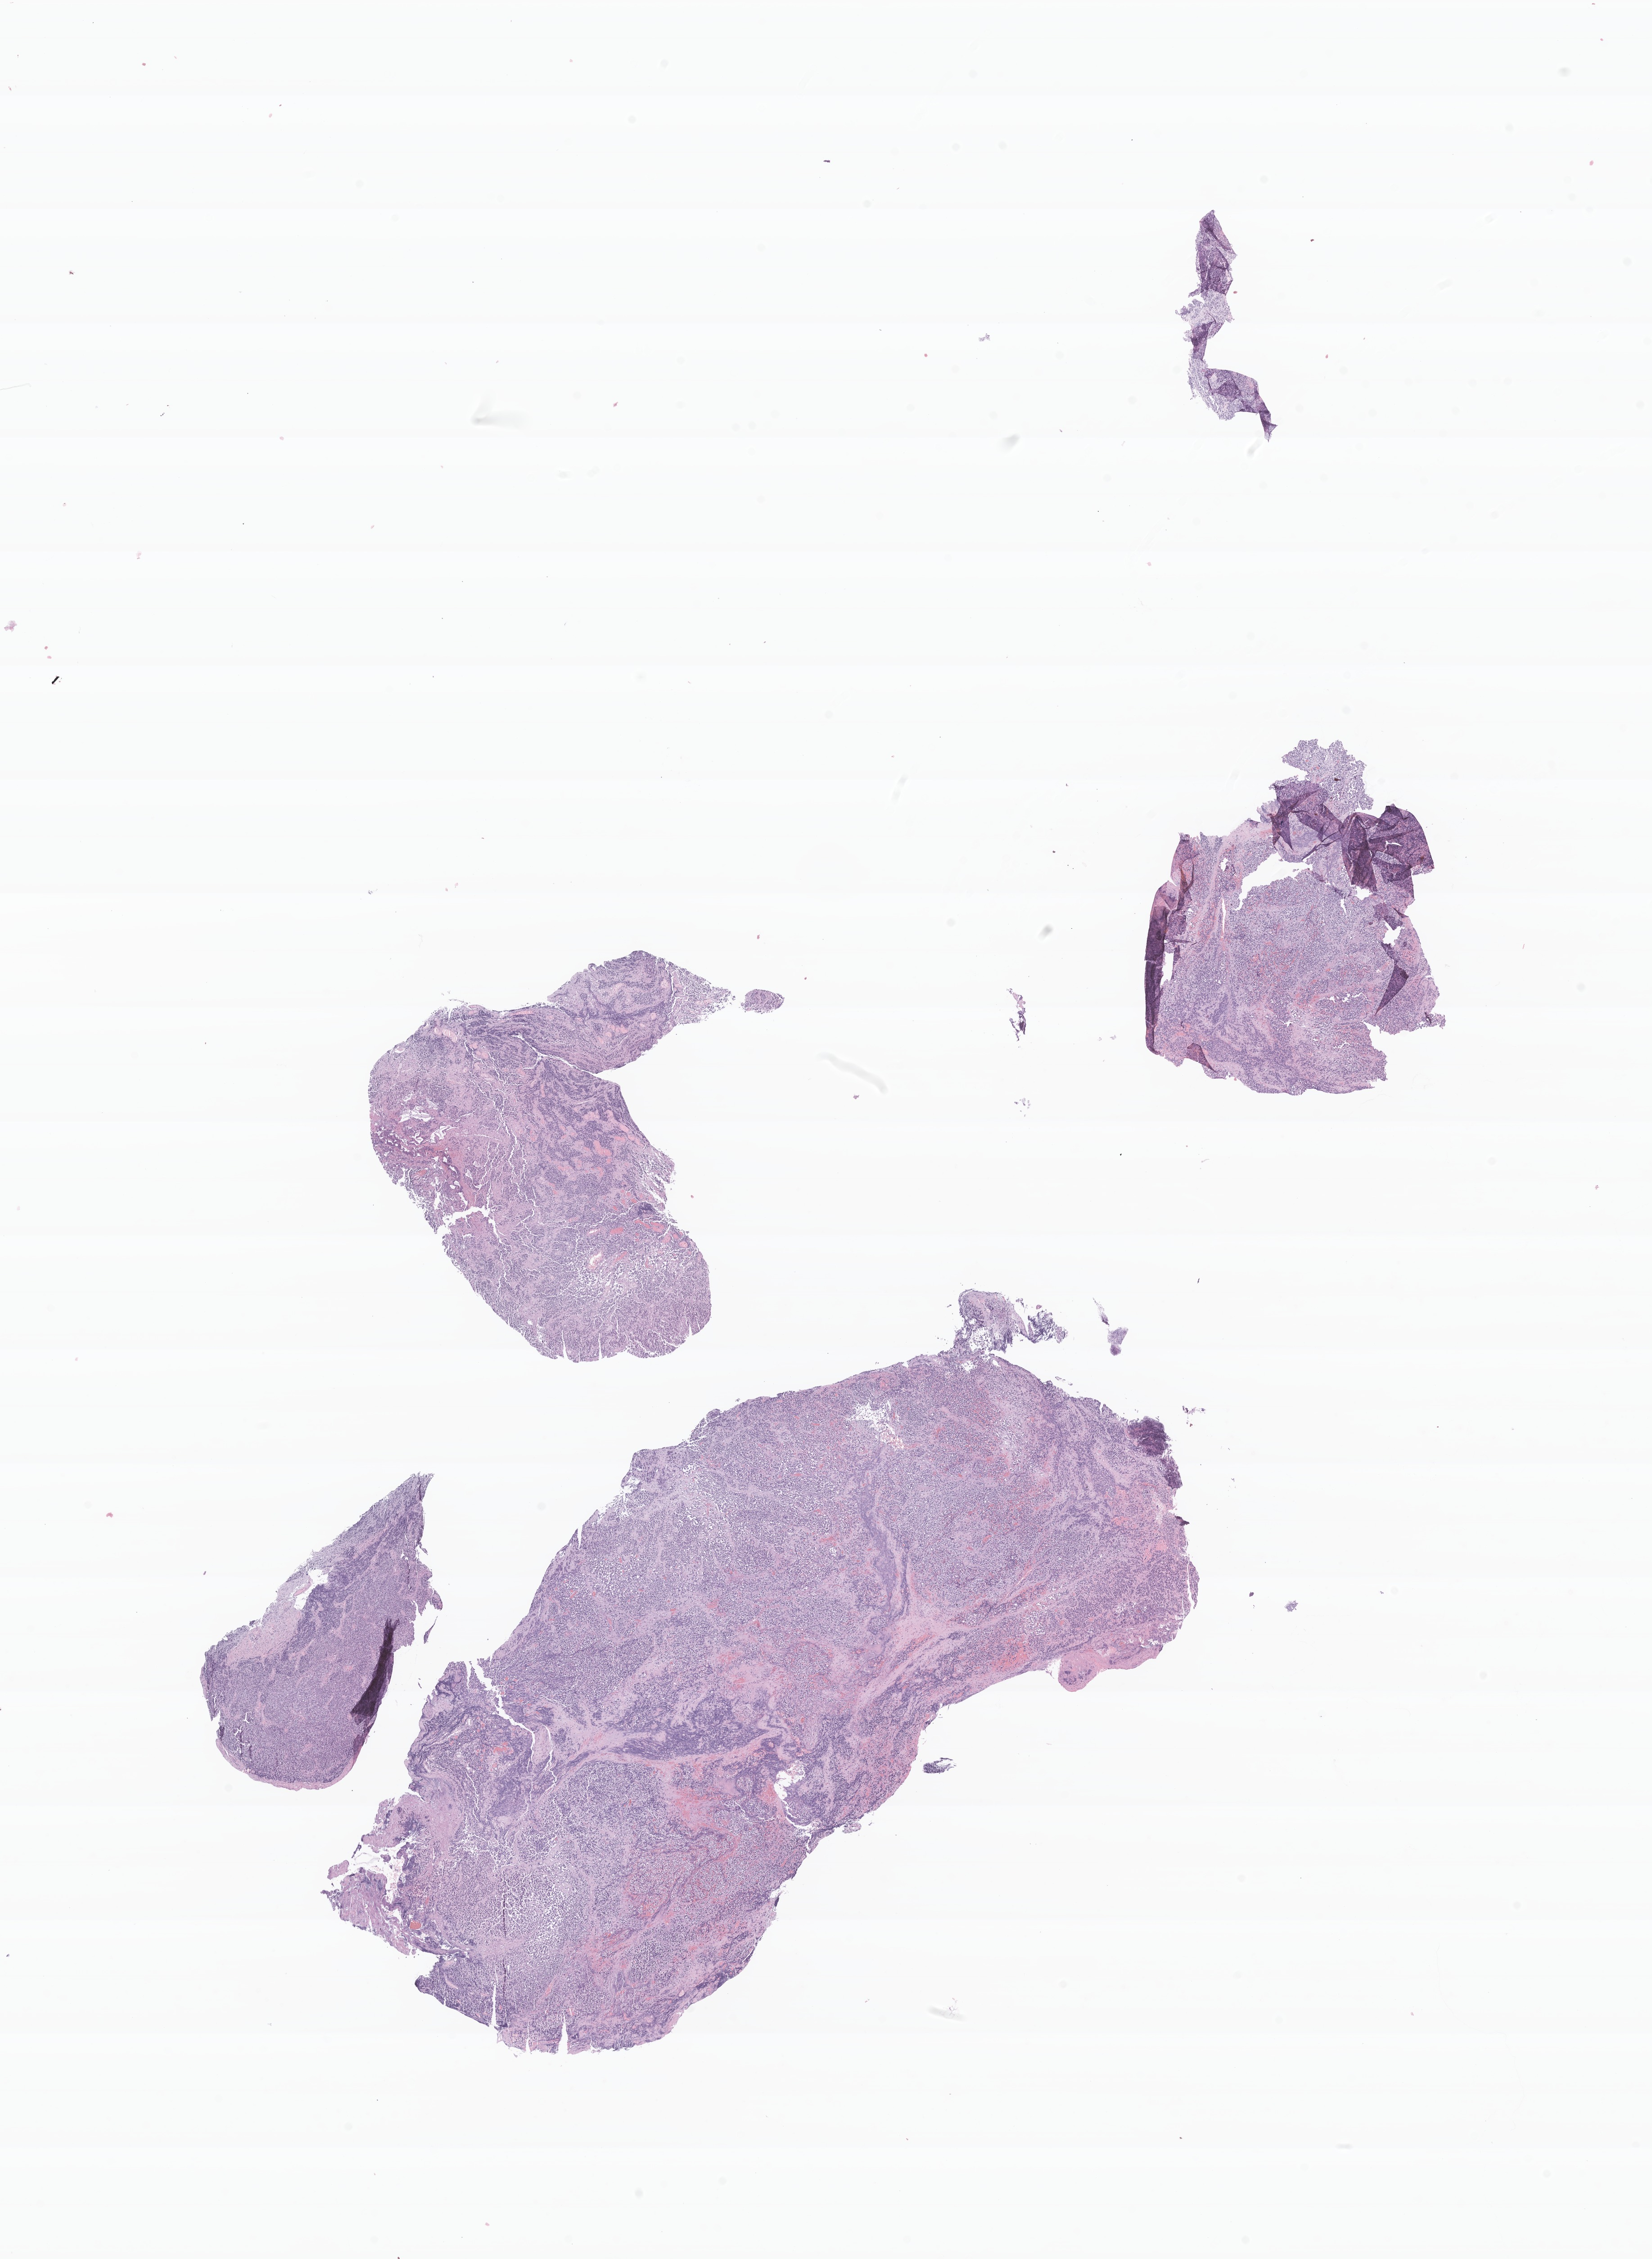
Hematoxylin and eosin (H&E) whole-slide image of tumor tissue from the brain, low-resolution overview of the scanned area, about 15.4 x 21.1 mm, formalin-fixed paraffin-embedded section. Female patient, age 89 months.
- diagnosis (ICD-O-3 morphology term): Pineoblastoma